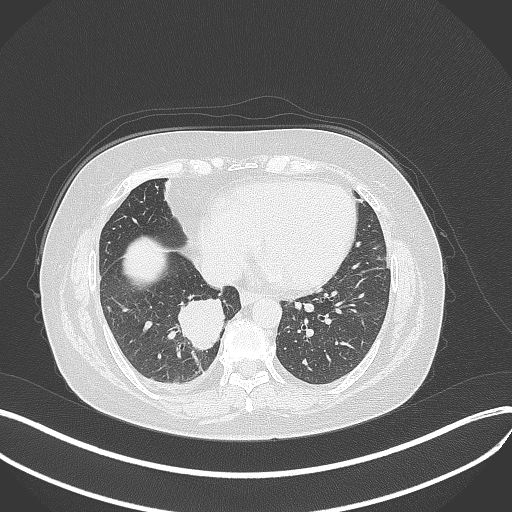
Chest CT, one axial slice; position 124 of 381 along the scan axis; lung window (W 1500 / L -600 HU); 1 mm slice thickness; 512 × 512 image matrix. Female patient, age 56 years. Case-level facts recorded for this patient, not image findings: clinical TNM (as recorded): T2b N1 M0.
Annotated regions visible in this slice (rectangle marked by the reading radiologist):
- lung tumour (recorded histology: small cell carcinoma): bounding box (x1, y1, x2, y2) in pixels: (174, 290, 228, 352)